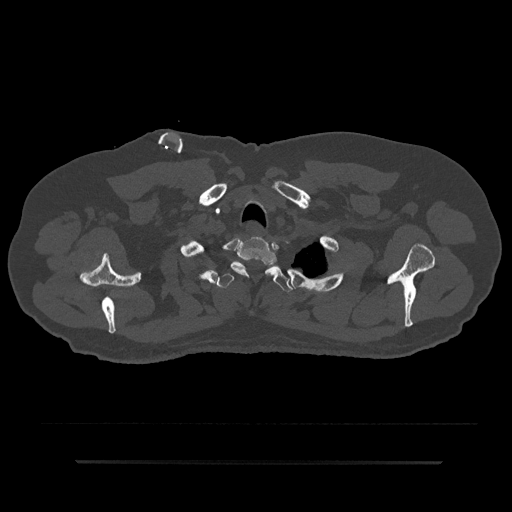
CT including the spine, one axial slice; reconstruction kernel Br40s/3; 120 kVp; bone window (W 1800 / L 400 HU); 512 × 512 image matrix. Patient: male, 59 years. From the clinical record (not read from this slice): primary cancer: bile ducts.
Outlined on this slice (semi-automatically segmented with operator editing):
- T1 vertebra: bounding box (x1, y1, x2, y2) in pixels: (230, 237, 278, 276)
- T2 vertebra: (215, 263, 293, 292)